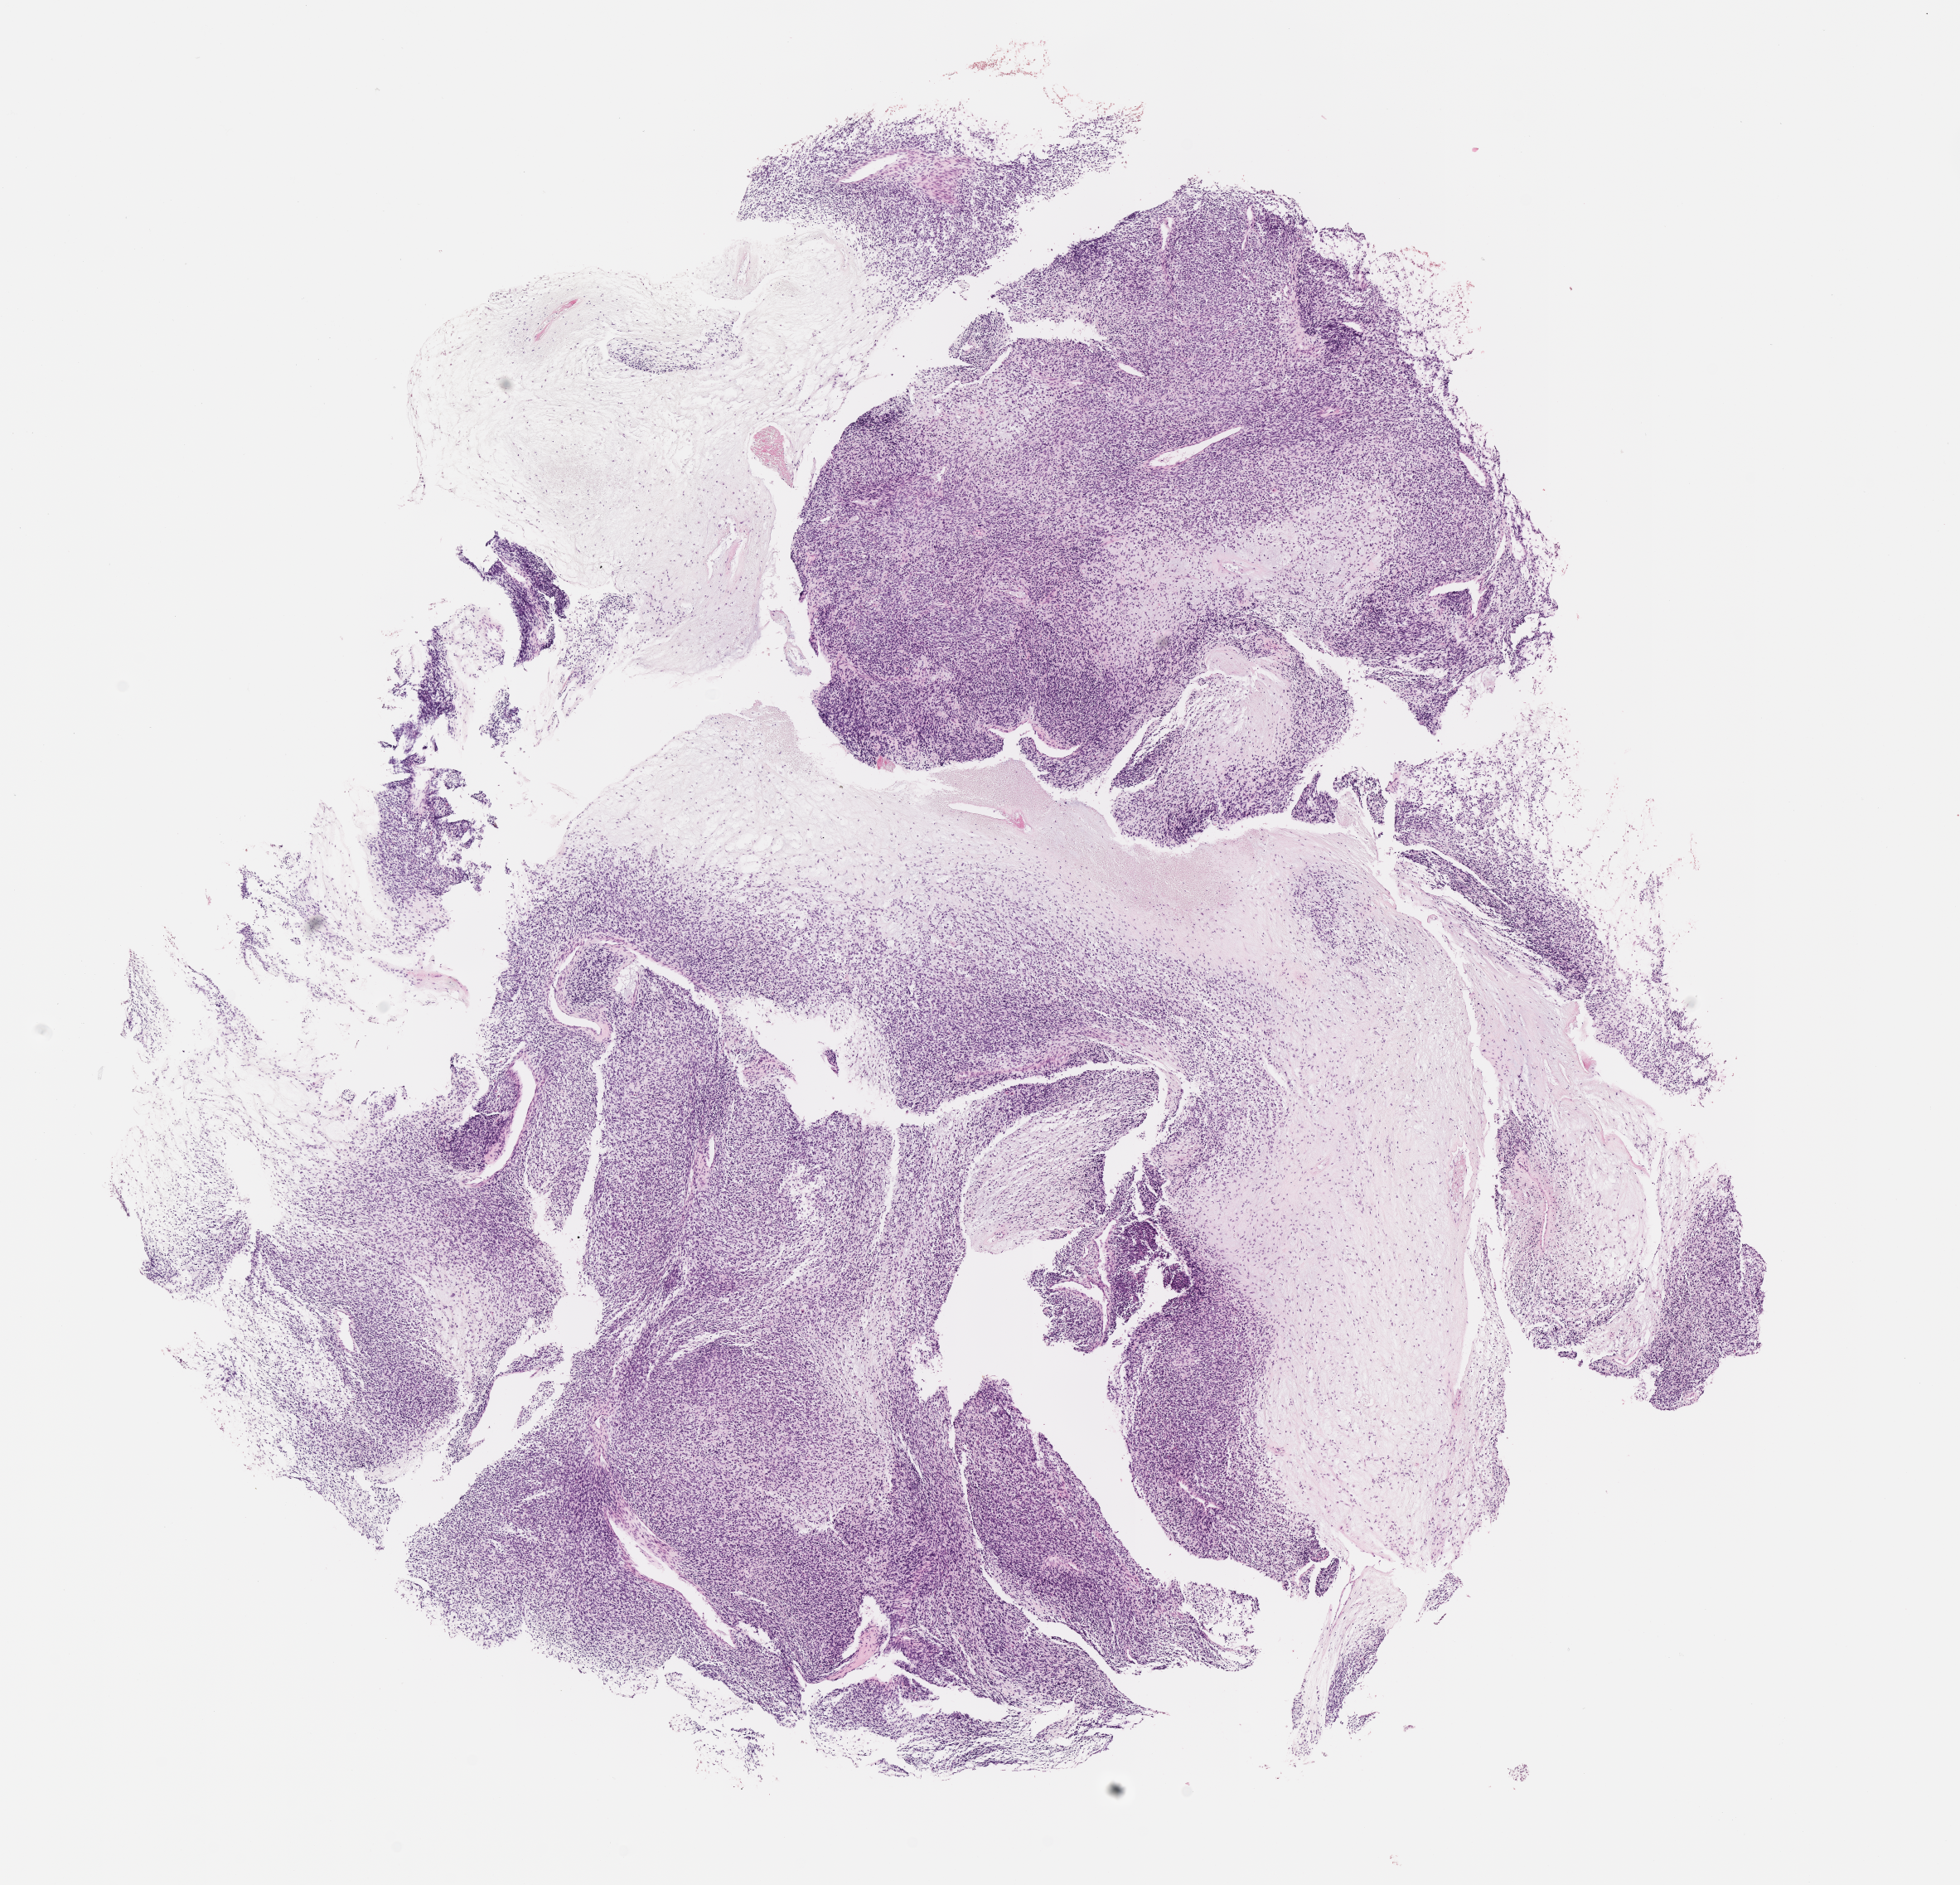
H&E whole-slide image of tumor tissue — whole scanned area (about 9.6 x 9.2 mm) shown as a low-resolution overview; formalin-fixed paraffin-embedded section. Patient: male, age 2.0 years at diagnosis.
Diagnosis: rhabdomyosarcoma; histological classification: embryonal rhabdomyosarcoma.